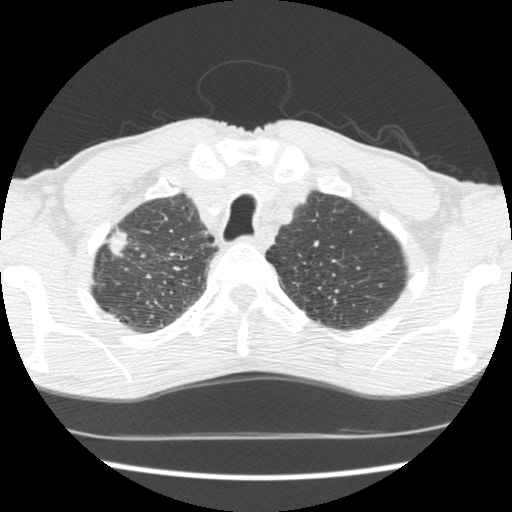
Low-dose screening chest CT, axial slice; baseline annual screen; lung window (W 1500 / L -600 HU); 2.5 mm slice thickness; standard (soft-tissue) reconstruction kernel (STANDARD); 120 kVp; slice 34 of 197 in the series; 512 × 512 image matrix. Male participant, aged 62 years at enrolment. Current smoker at enrolment.
Lesion marked by an expert reader, box from (x=90, y=223) to (x=142, y=274) px. Screening reader's record for this exam: no non-calcified nodule ≥4 mm recorded. Official screen result: negative screen, significant abnormalities not suspicious for lung cancer. Participant outcome: lung cancer diagnosed 640 days after this screen — adenocarcinoma, NOS, right upper lobe, poorly differentiated (G3), stage IIA (AJCC 6th edition), 22 mm at pathology.